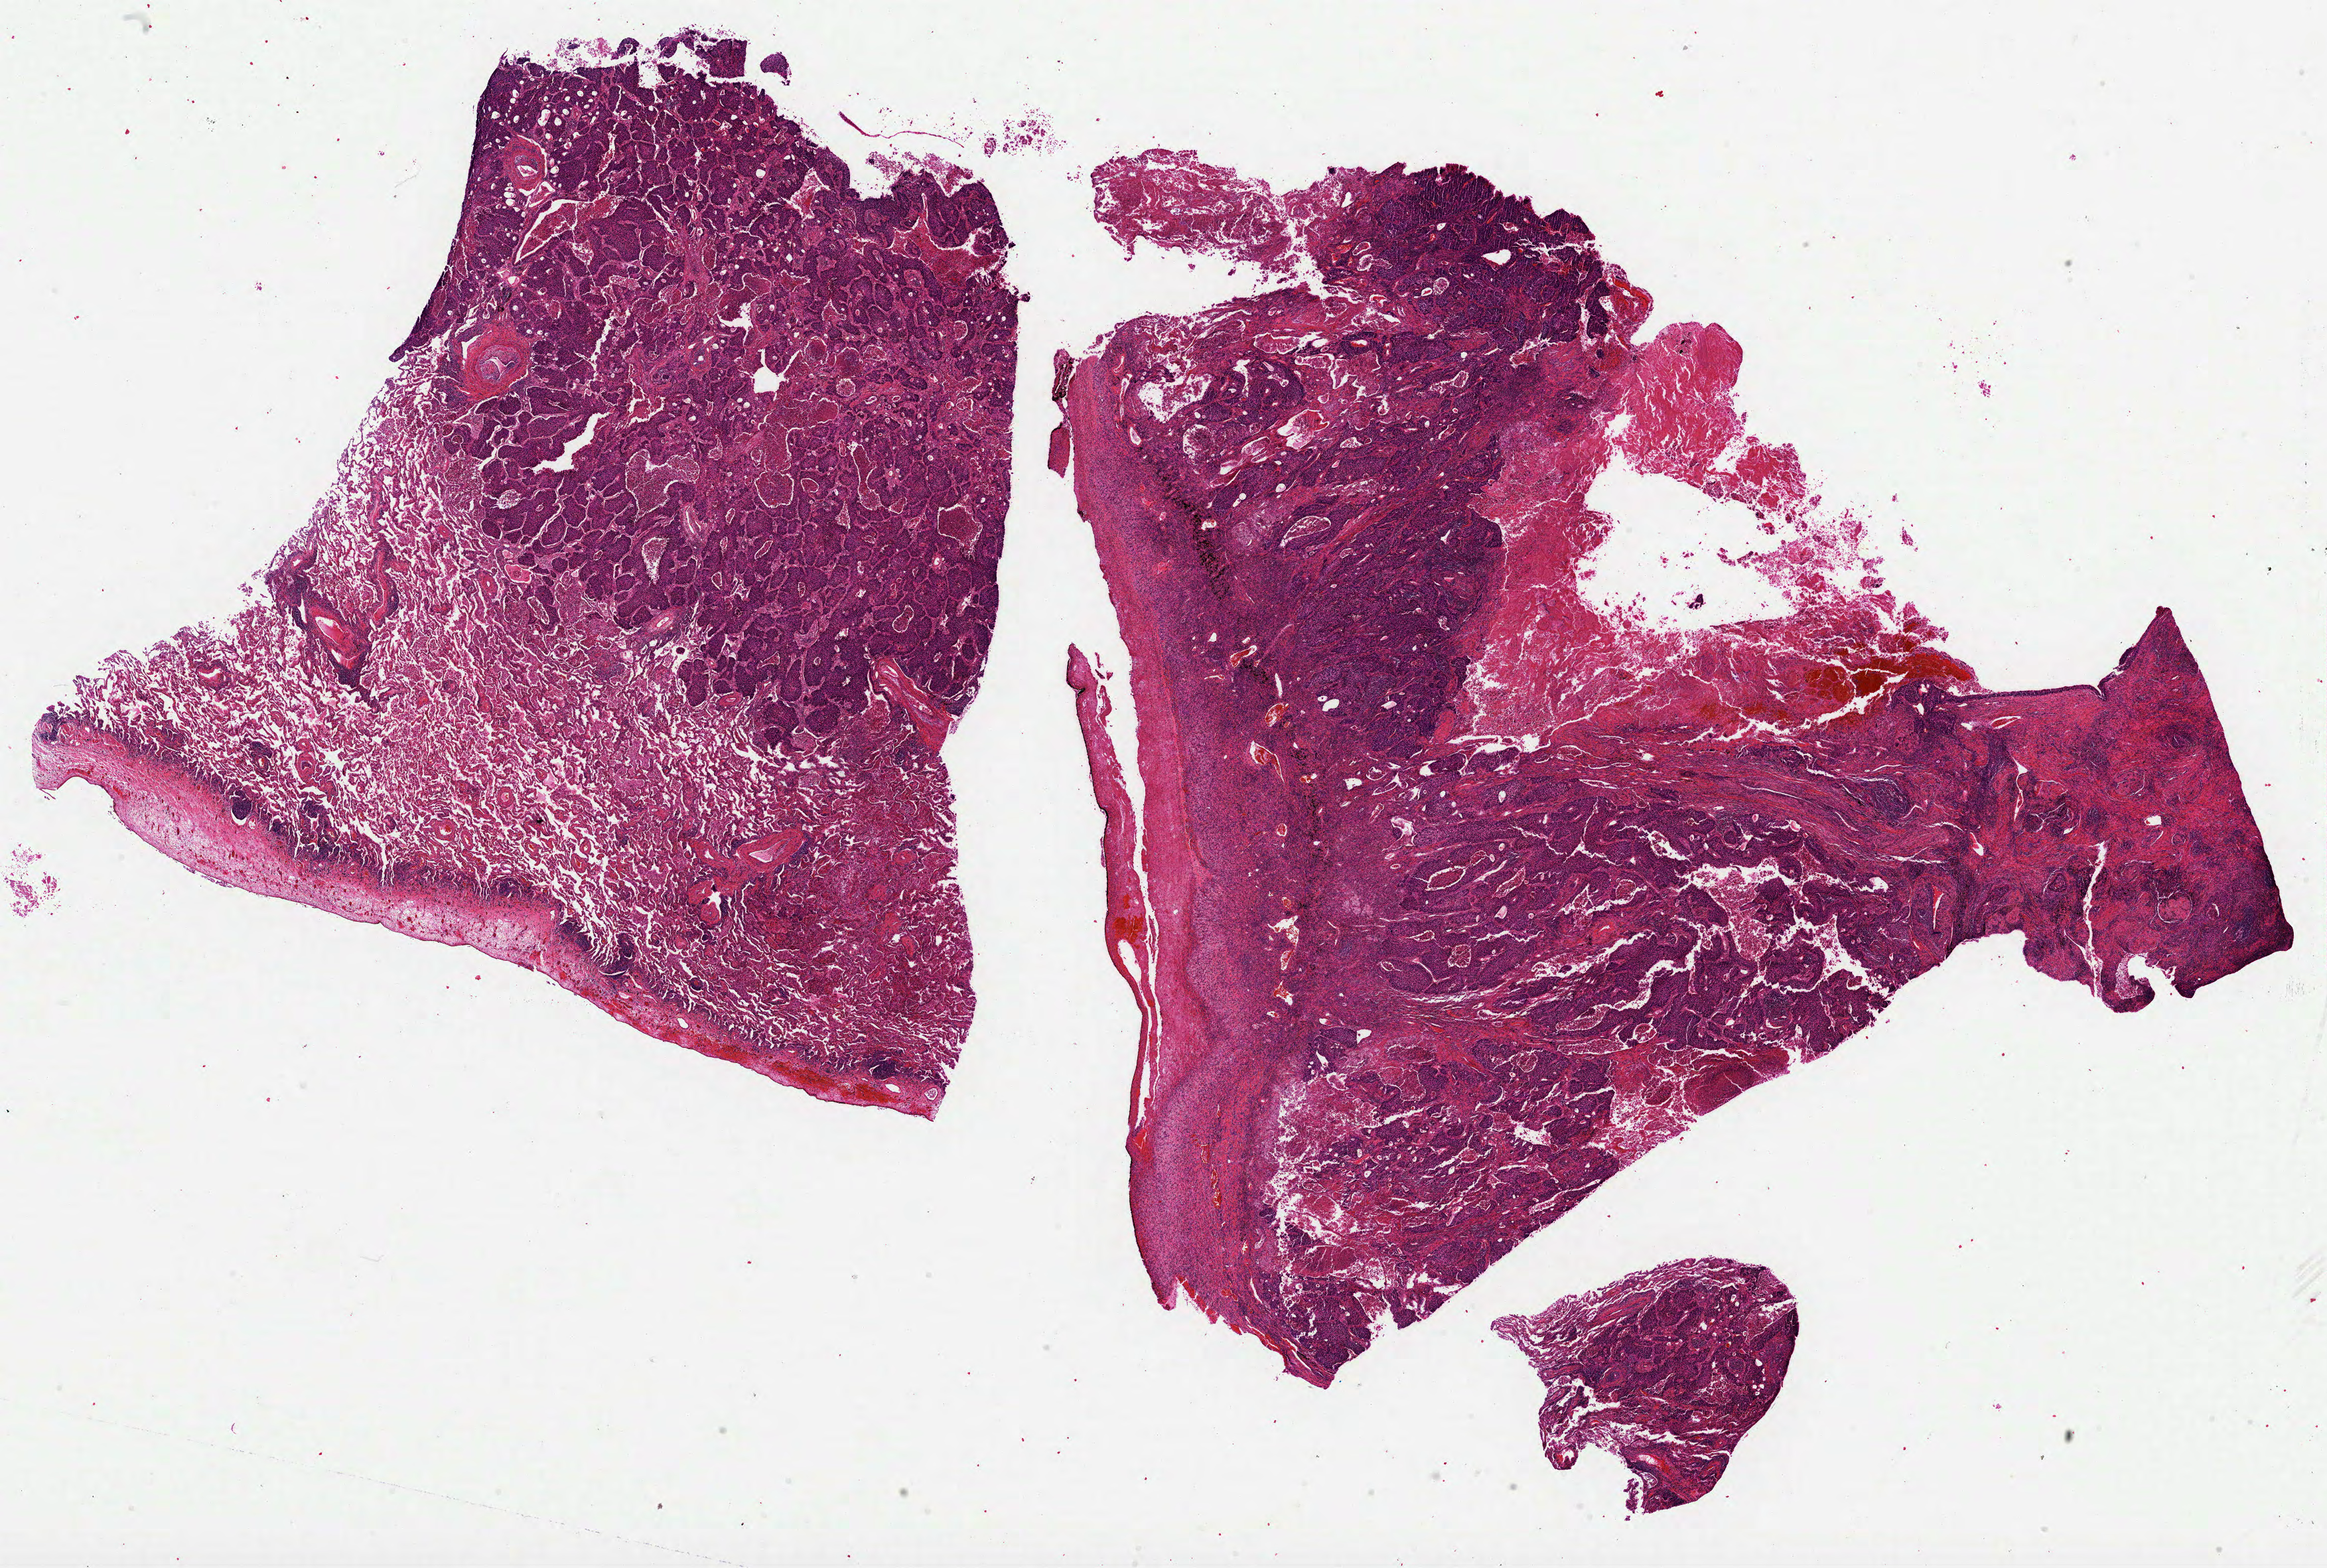
Whole-slide histology image, Hematoxylin and eosin (H&E) stained — a low-resolution overview of the entire scanned area, about 28.3 x 19.1 mm (acquisition: 40x scan). Formalin-fixed paraffin-embedded (FFPE) diagnostic section. Primary tumour sample from the lung. Male patient; age at initial diagnosis 68 years.
Histologic diagnosis: Squamous cell carcinoma, NOS (lower lobe, lung).